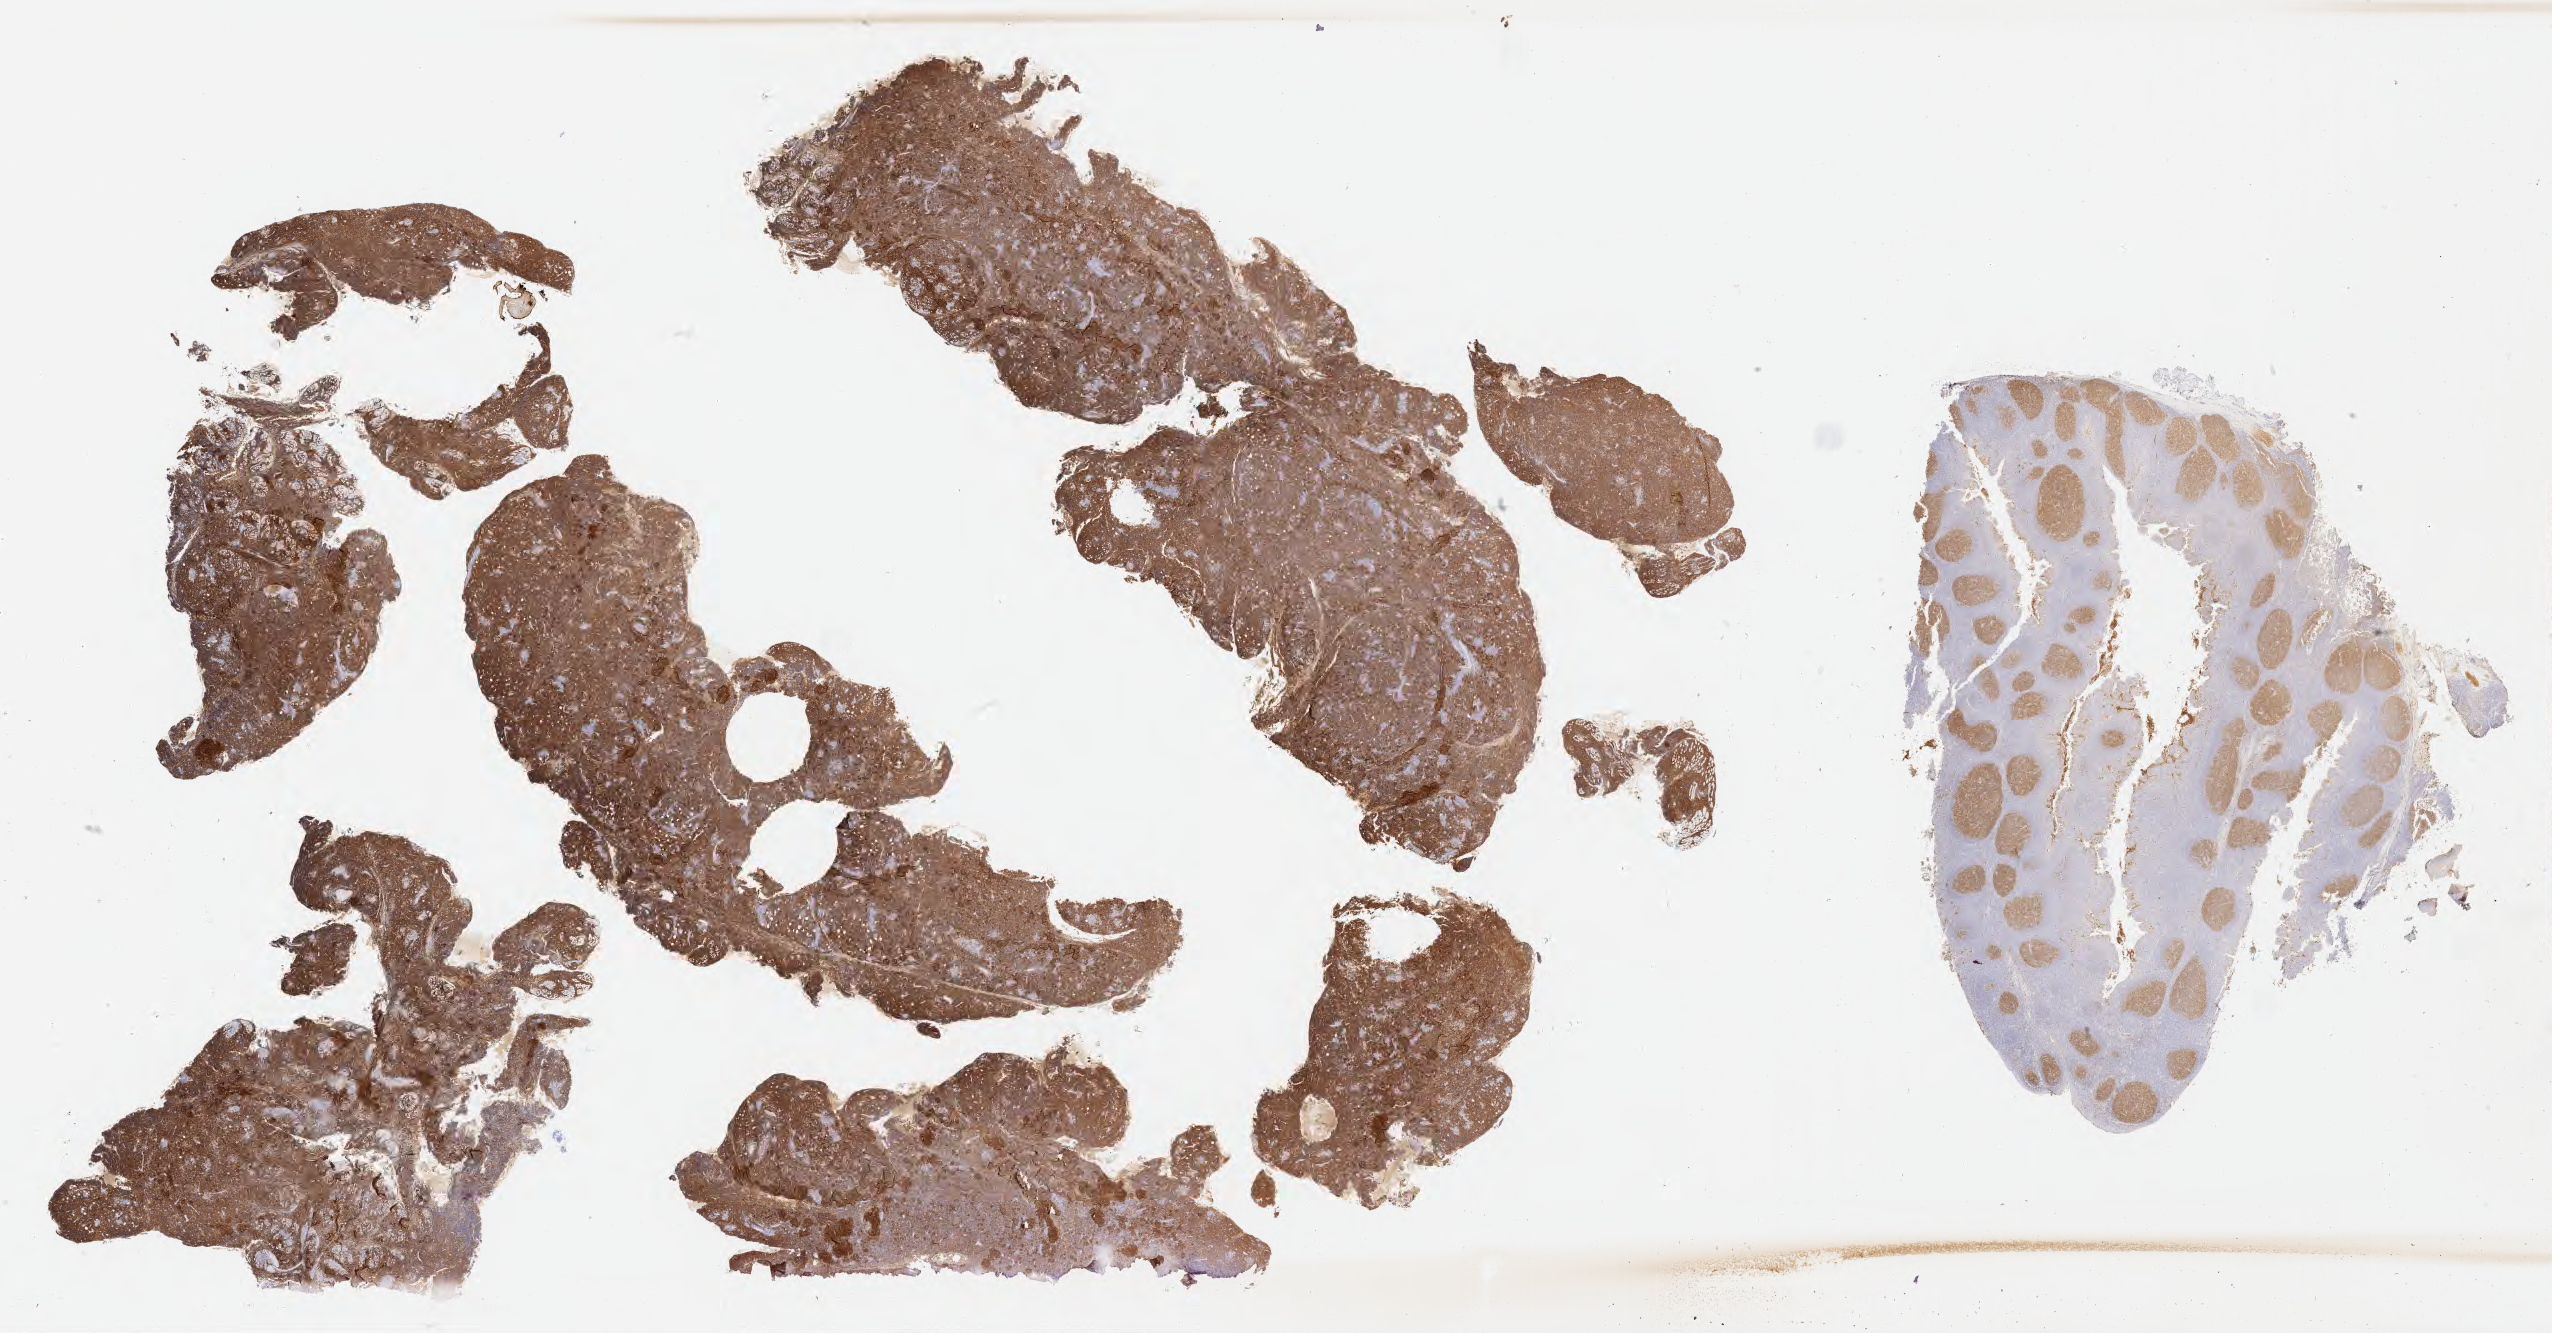
Immunohistochemistry (IHC) whole-slide image stained for CD10 — shown as a low-resolution overview of the whole scanned area (about 41.3 x 21.6 mm); tumor tissue; site: cranium. Male, age 5 years at initial diagnosis.
Diagnosis: Burkitt lymphoma, NOS.